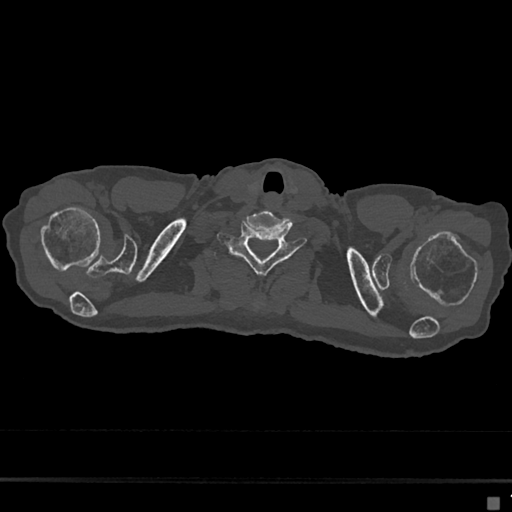
CT including the spine, one axial slice; position 637 of 797 along the scan axis; reconstruction kernel Br40s/3; bone window (W 1800 / L 400 HU); 0.5 mm slice thickness; 512 × 512 image matrix, field of view 360 × 360 mm. Patient: female, 68 years. Case-level facts recorded for this patient, not image findings: primary cancer: renal.
Annotated regions visible in this slice (semi-automatically segmented with operator editing):
- T1 vertebra: bounding box (x1, y1, x2, y2) in pixels: (214, 252, 217, 259)